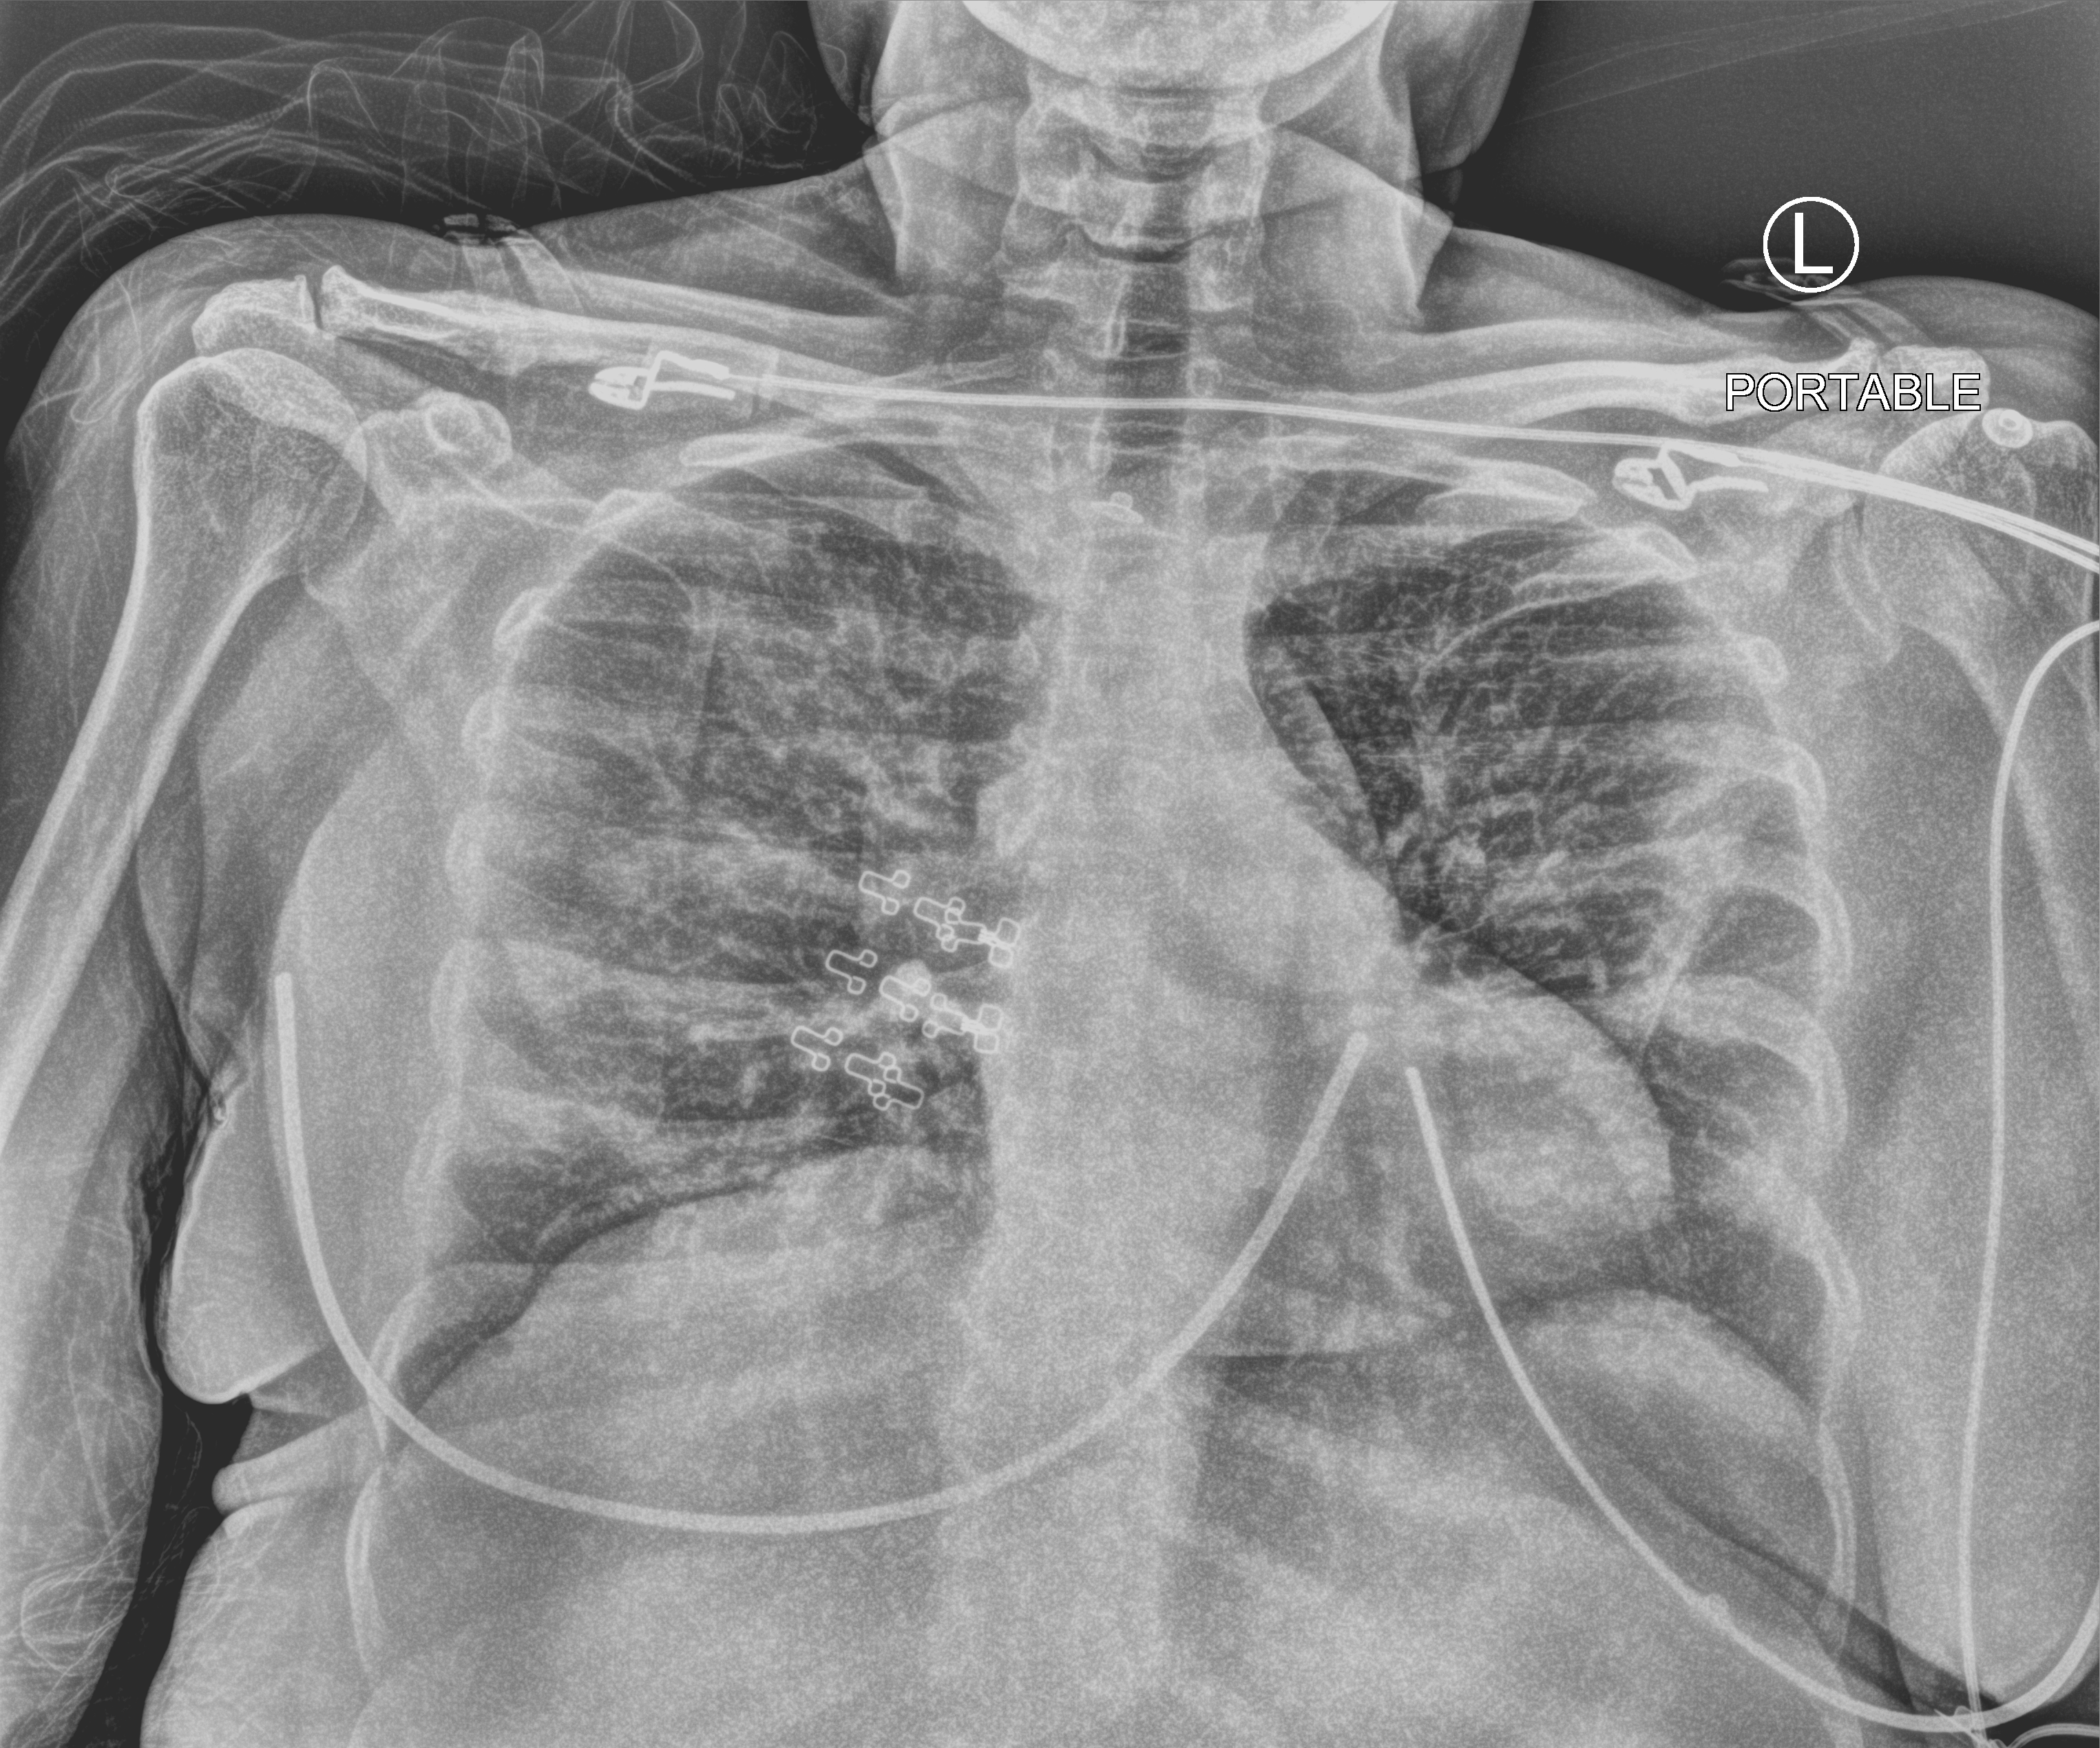
Chest X-ray (portable). Female patient hospitalised with COVID-19, age 18–59 years.
From the hospital-stay record, not from the radiograph (when in the stay this image was taken is not recorded): mechanically ventilated during this hospital stay: no; hypertension (admission record): no.